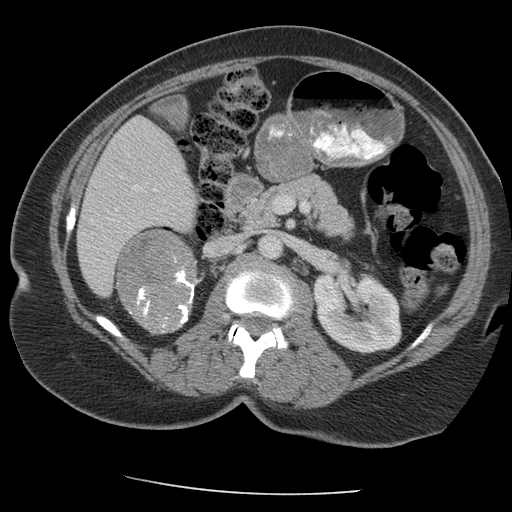
Contrast-enhanced abdominal CT, one axial slice; position 113 of 163 along the scan axis; reconstruction kernel STANDARD; 140 kVp; intravenous contrast given; soft-tissue window (W 400 / L 40 HU); 2.5 mm slice thickness; 512 × 512 image matrix, field of view 360 × 360 mm. Female patient, age 70 years. From the clinical record (not read from this slice): diagnosis: adrenocortical carcinoma; tumour side: right adrenal; tumour size at pathology: 9.5 cm; Ki-67 index: 5 %; stage (as recorded): 2.
Structures marked on this image (semi-automatically segmented with operator editing):
- mass: box from (x=117, y=230) to (x=197, y=333) px